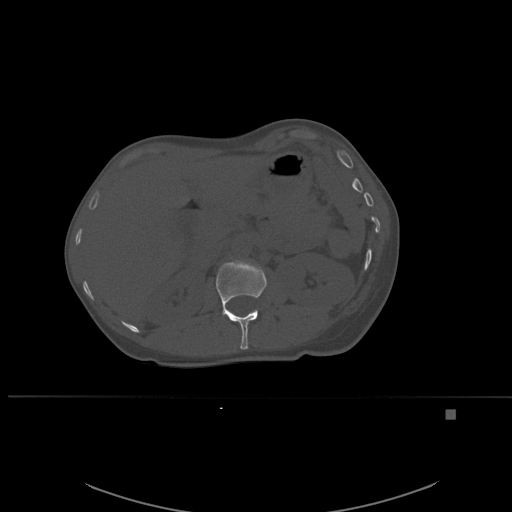
CT including the spine, one axial slice; position 256 of 537 along the scan axis; bone window (W 1800 / L 400 HU); 1.5 mm slice thickness; 512 × 512 image matrix, field of view 440 × 440 mm. Female patient, age 45 years. From the clinical record (not read from this slice): primary cancer: lung.
Outlined on this slice (semi-automatically segmented with operator editing):
- L1 vertebra: bounding box (x1, y1, x2, y2) in pixels: (216, 260, 267, 350)